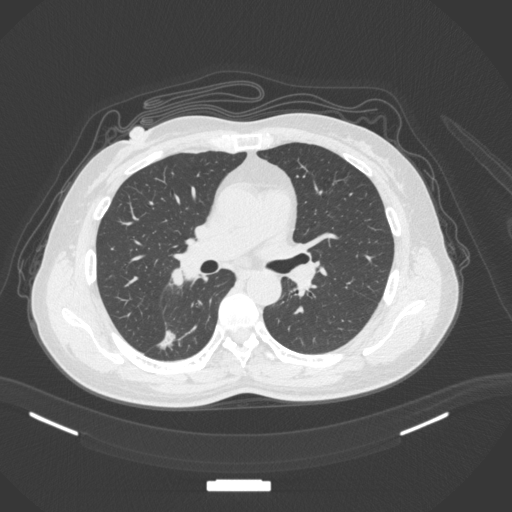
Chest CT, one axial slice. Slice 176 of 352 in the series (ordered by position). Reconstruction kernel B31f. 120 kVp. Lung window (W 1500 / L -600 HU). 1 mm slice thickness. 512 × 512 image matrix, field of view 400 × 400 mm. Female patient, age 55 years. Case-level facts recorded for this patient, not image findings: clinical TNM (as recorded): T1c N1 M0.
Structures marked on this image (bounding box drawn by a radiologist):
- lung tumour (recorded histology: adenocarcinoma): box from (x=155, y=325) to (x=181, y=352) px